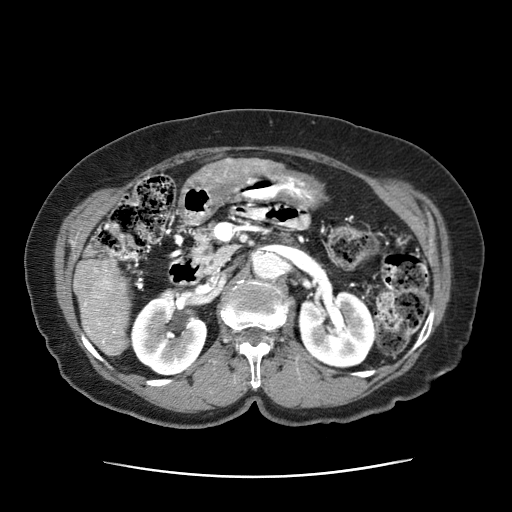
Contrast-enhanced abdominal CT (liver protocol), one axial slice. Slice 16 of 63 in the series (ordered by position). 120 kVp. Intravenous contrast given. Soft-tissue window (W 400 / L 40 HU). 2.5 mm slice thickness. 512 × 512 image matrix, field of view 360 × 360 mm. Patient: female, 79 years. From the clinical record (not read from this slice): diagnosis: hepatocellular carcinoma (patient treated with transarterial chemoembolisation; whether this scan precedes or follows treatment is not stated here); TNM stage (as recorded): Stage-II; Child-Pugh class: B; tumour nodularity: multinodular.
Outlined on this slice (semi-automatic segmentation, software-assisted and operator-edited):
- abdominal aorta: bounding box (x1, y1, x2, y2) in pixels: (254, 250, 284, 278)
- liver parenchyma outside the tumour (the mass and vessels are separate outlines, so this box may not span the whole liver): (73, 253, 133, 358)
- mass: (190, 158, 260, 179)
- liver vessels: (84, 269, 108, 344)